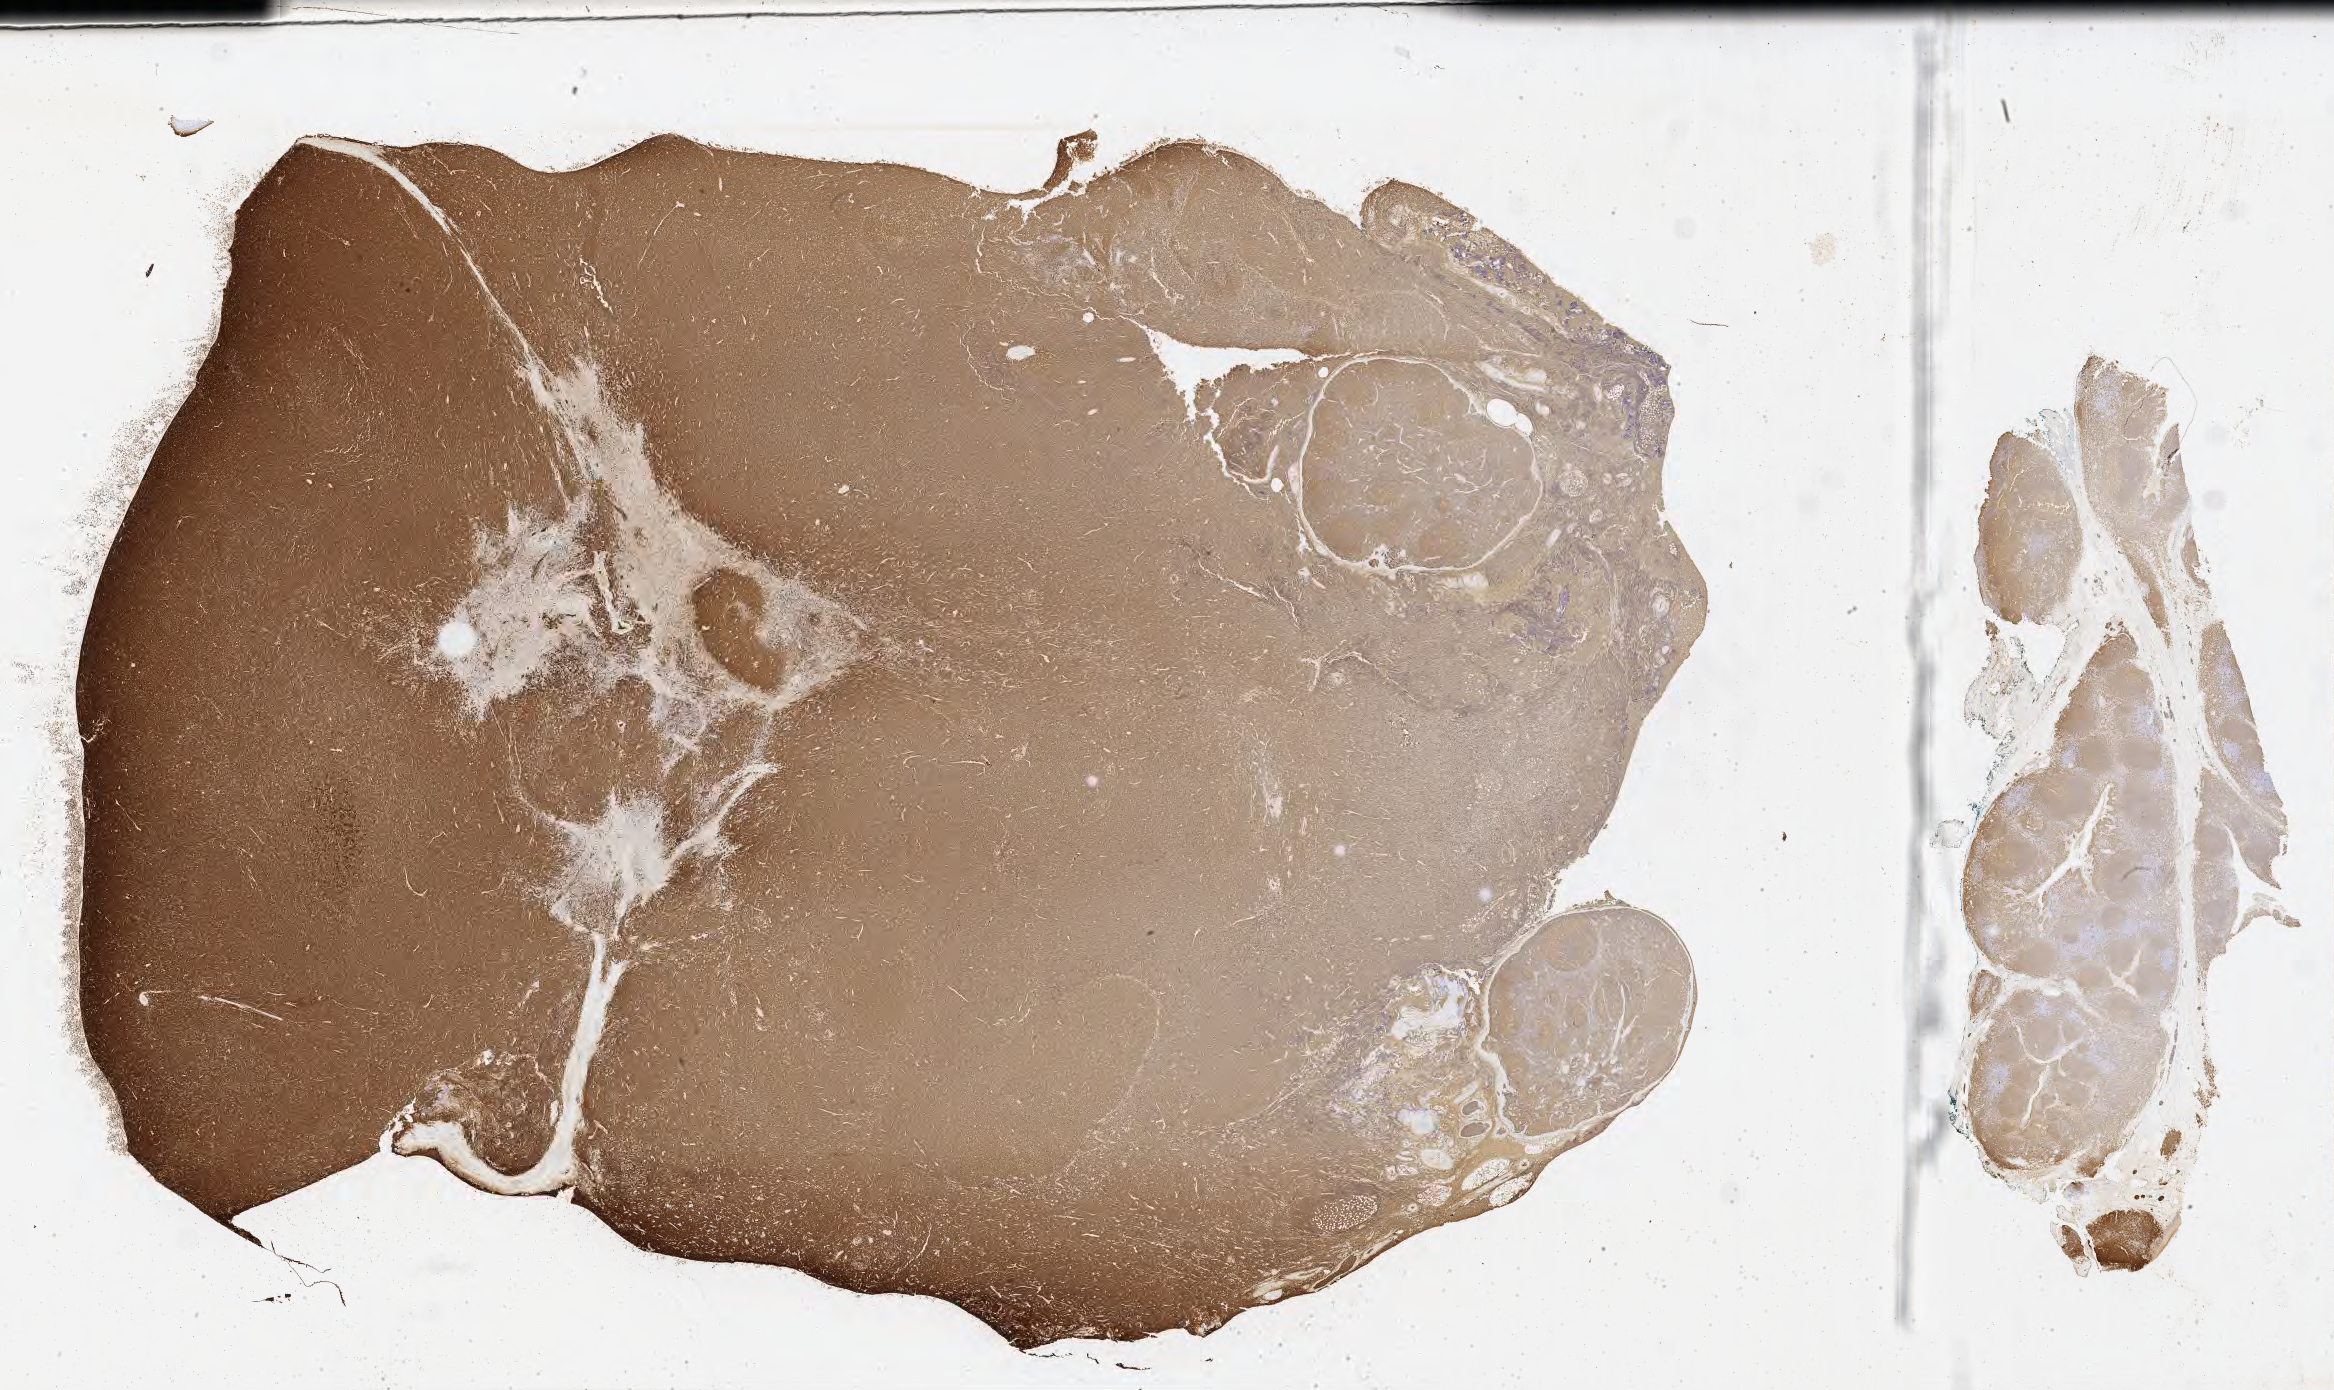
Whole-slide image, immunohistochemical stain for CD20, shown as a low-resolution overview of the whole scanned area (about 37.7 x 22.5 mm), tumor tissue, anatomic site: lymph node of head and neck. Patient: male, age at initial diagnosis 3 years.
• histologic diagnosis: Burkitt lymphoma, NOS